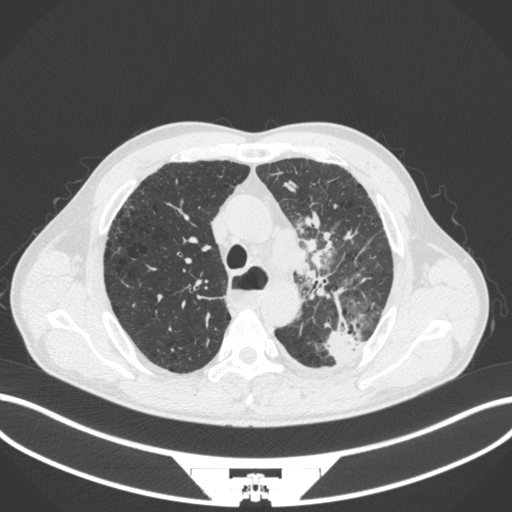
Chest CT, one axial slice; slice 283 of 411 in the series (ordered by position); lung window (W 1500 / L -600 HU); 512 × 512 image matrix, field of view 400 × 400 mm. Patient: male, 57 years. Case-level facts recorded for this patient, not image findings: clinical TNM (as recorded): T2a N1 M0.
Structures marked on this image (rectangle marked by the reading radiologist):
- lung tumour (recorded histology: squamous cell carcinoma): bounding box (x1, y1, x2, y2) in pixels: (290, 233, 322, 282)